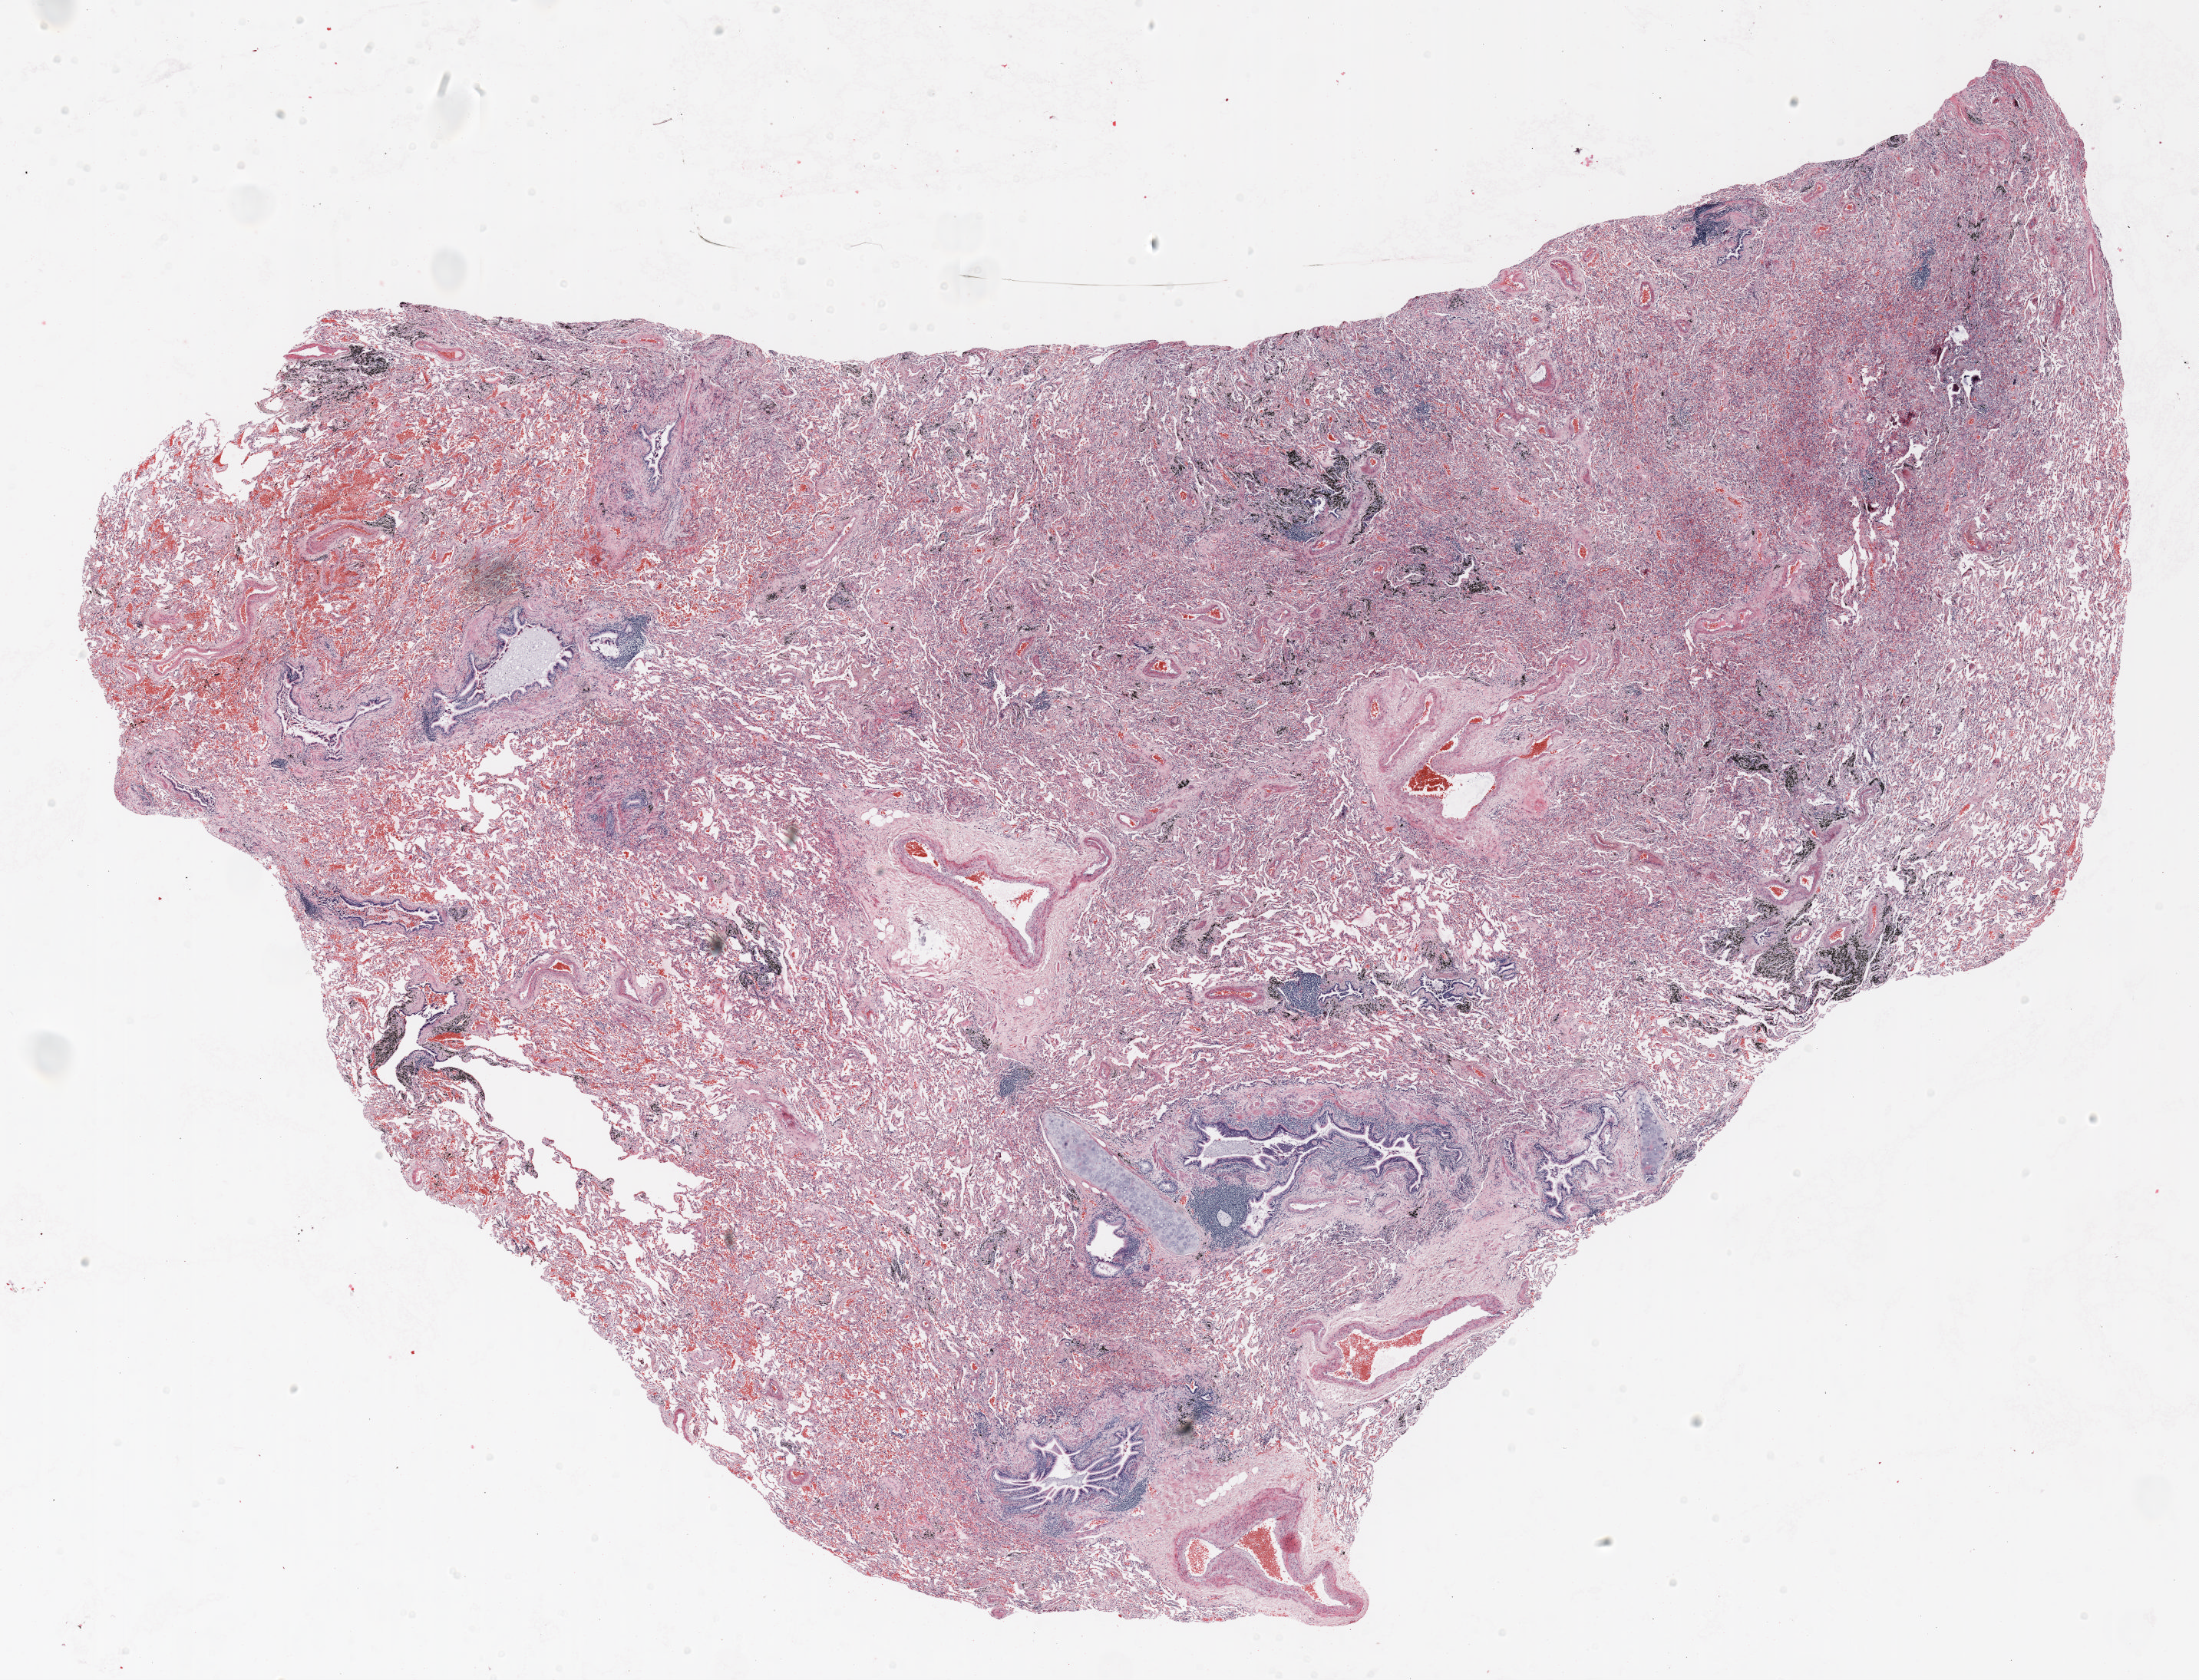
H&E-stained whole-slide image, low-resolution overview of the scanned area, about 23.0 x 17.6 mm (acquisition: 20x scan); FFPE section; lung. Male, age 59 at enrolment. Former smoker at enrolment. Grade: moderately differentiated (G2).
Stage (AJCC 6th edition): IA. Tumour size (pathology): 27 mm. ICD-O-3 topography: upper lobe of lung (C34.1). Participant's lung-cancer diagnosis: Squamous cell carcinoma, NOS (ICD-O-3 8070/3). Primary tumour location (clinical record): left upper lobe.